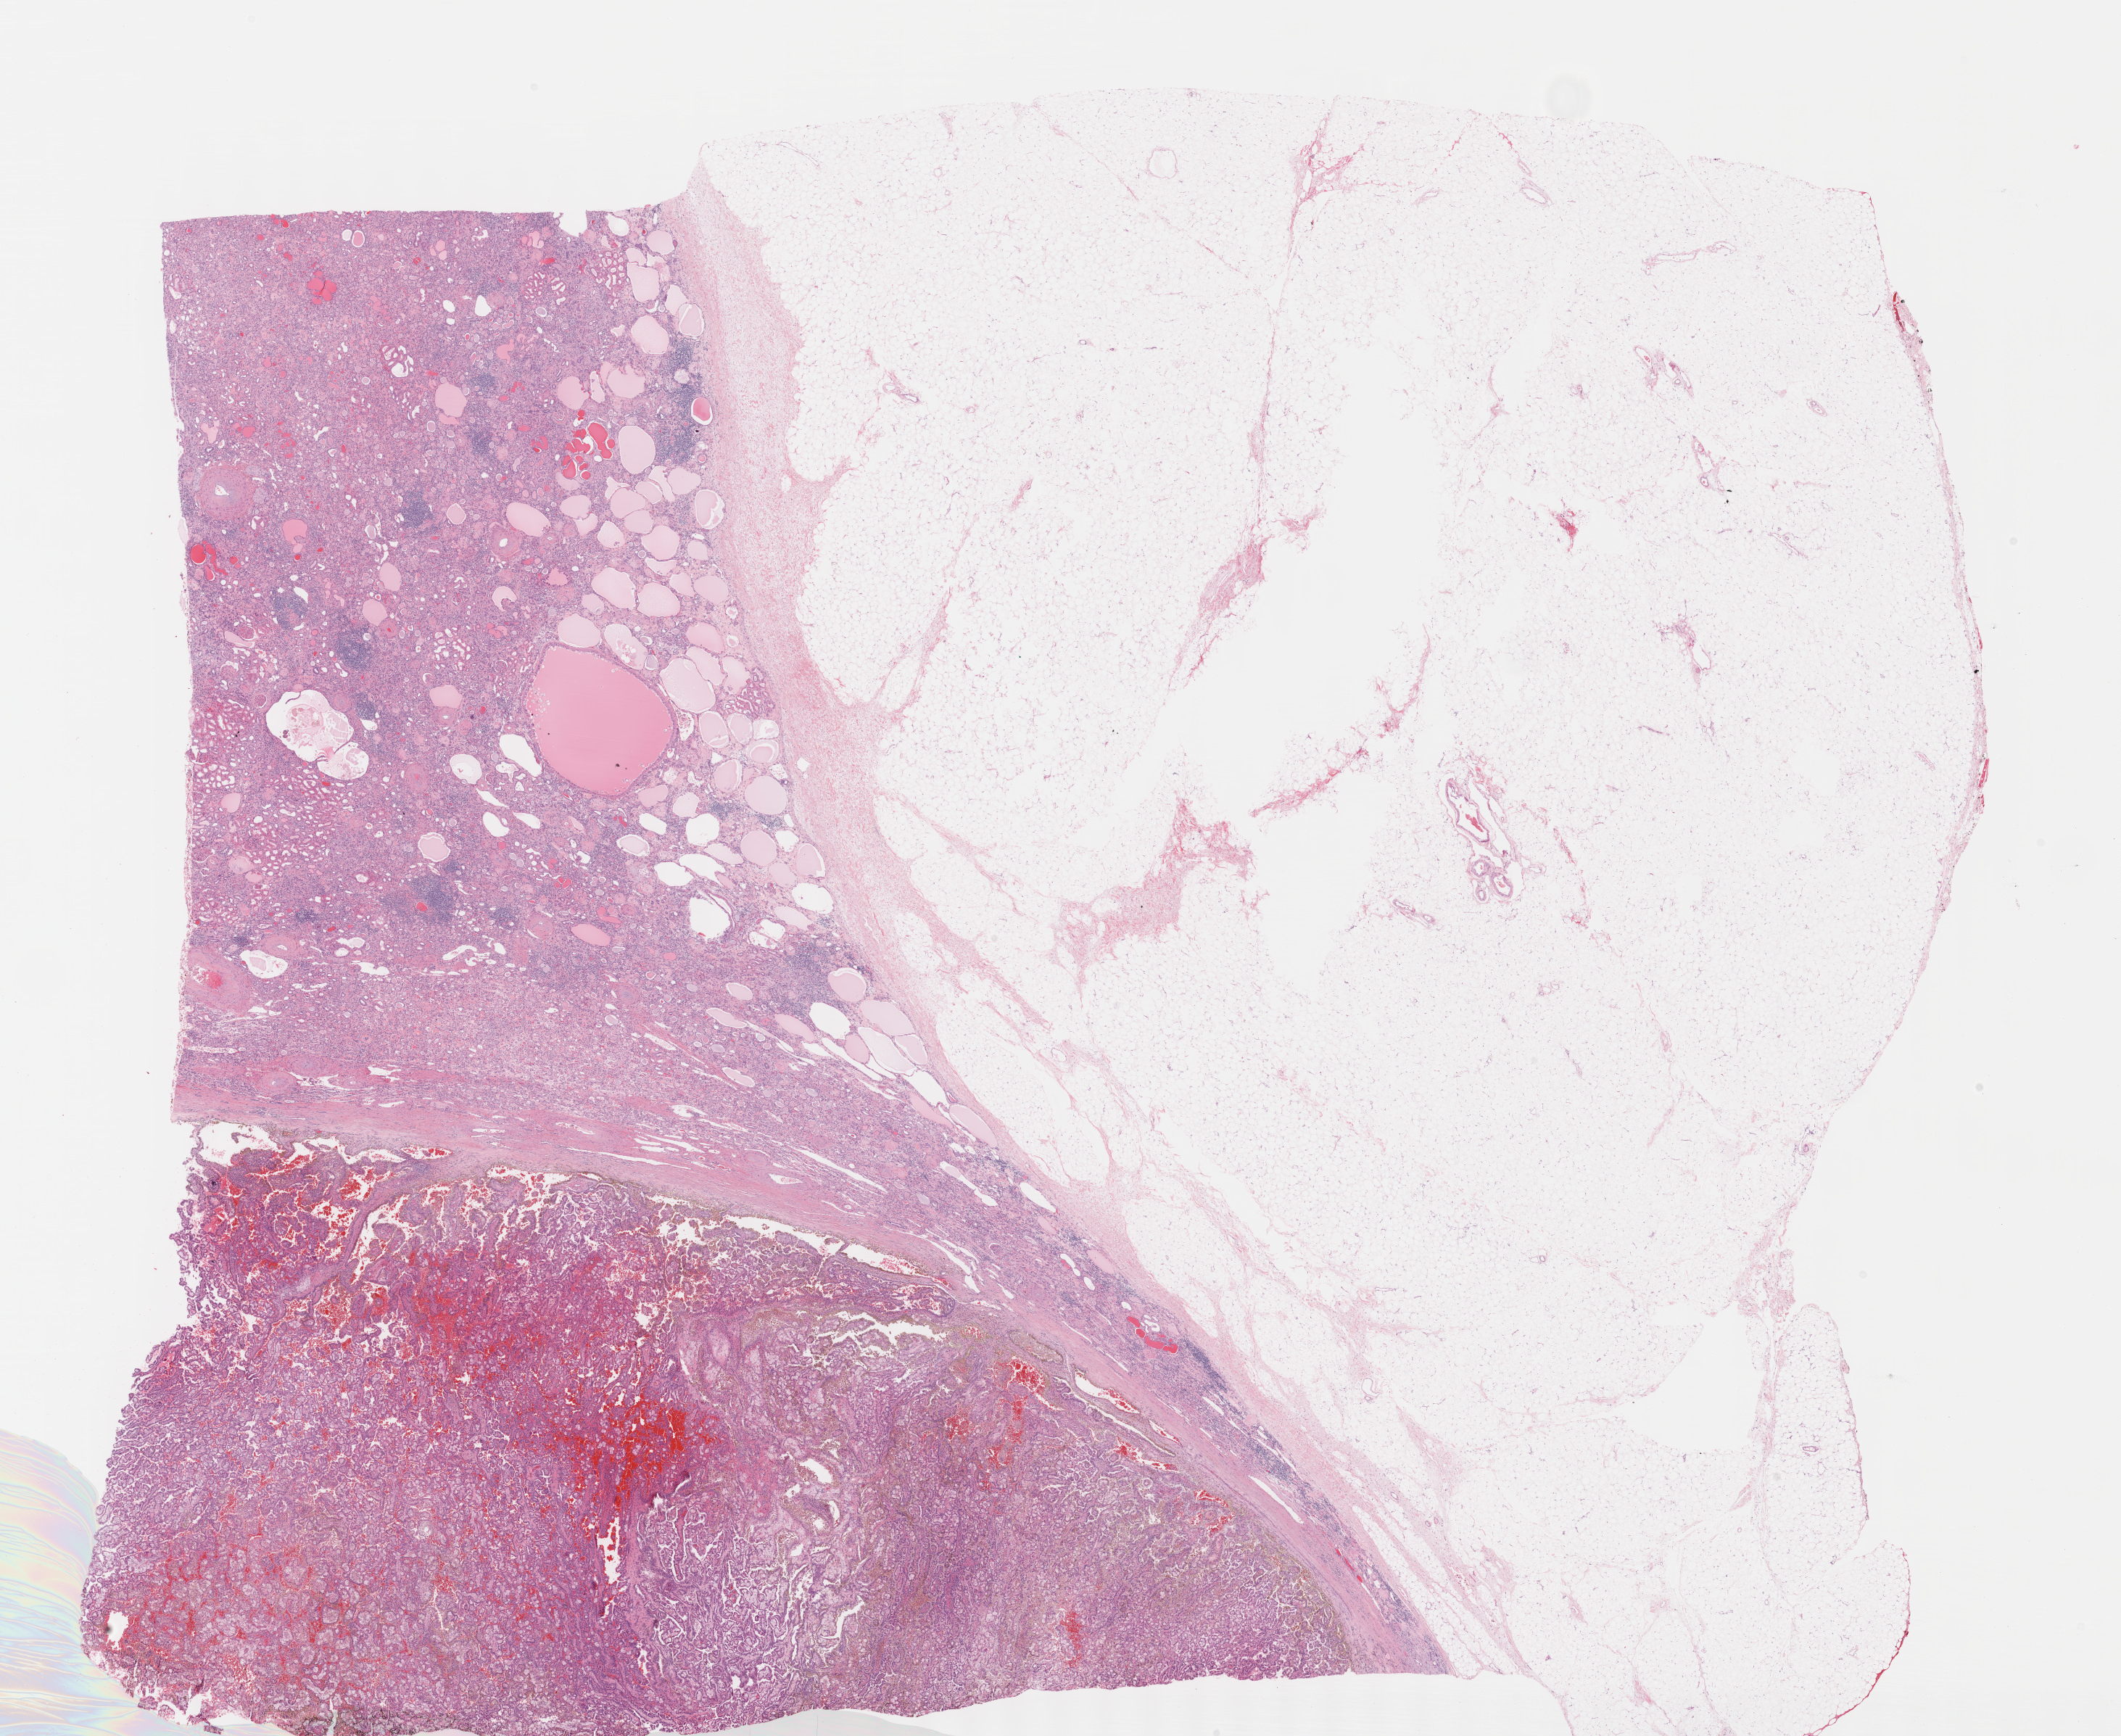
Digitized Hematoxylin and eosin (H&E) stained tissue section (whole slide), whole scanned area (about 23.6 x 19.3 mm, acquisition: 40x scan) shown as a low-resolution overview. Formalin-fixed paraffin-embedded (FFPE) diagnostic section. Primary tumour sample from the kidney. Male, age 73 years at initial diagnosis.
Histologic diagnosis: Papillary adenocarcinoma, NOS. TNM: T1 N0 MX. AJCC pathologic stage: I (6th edition).